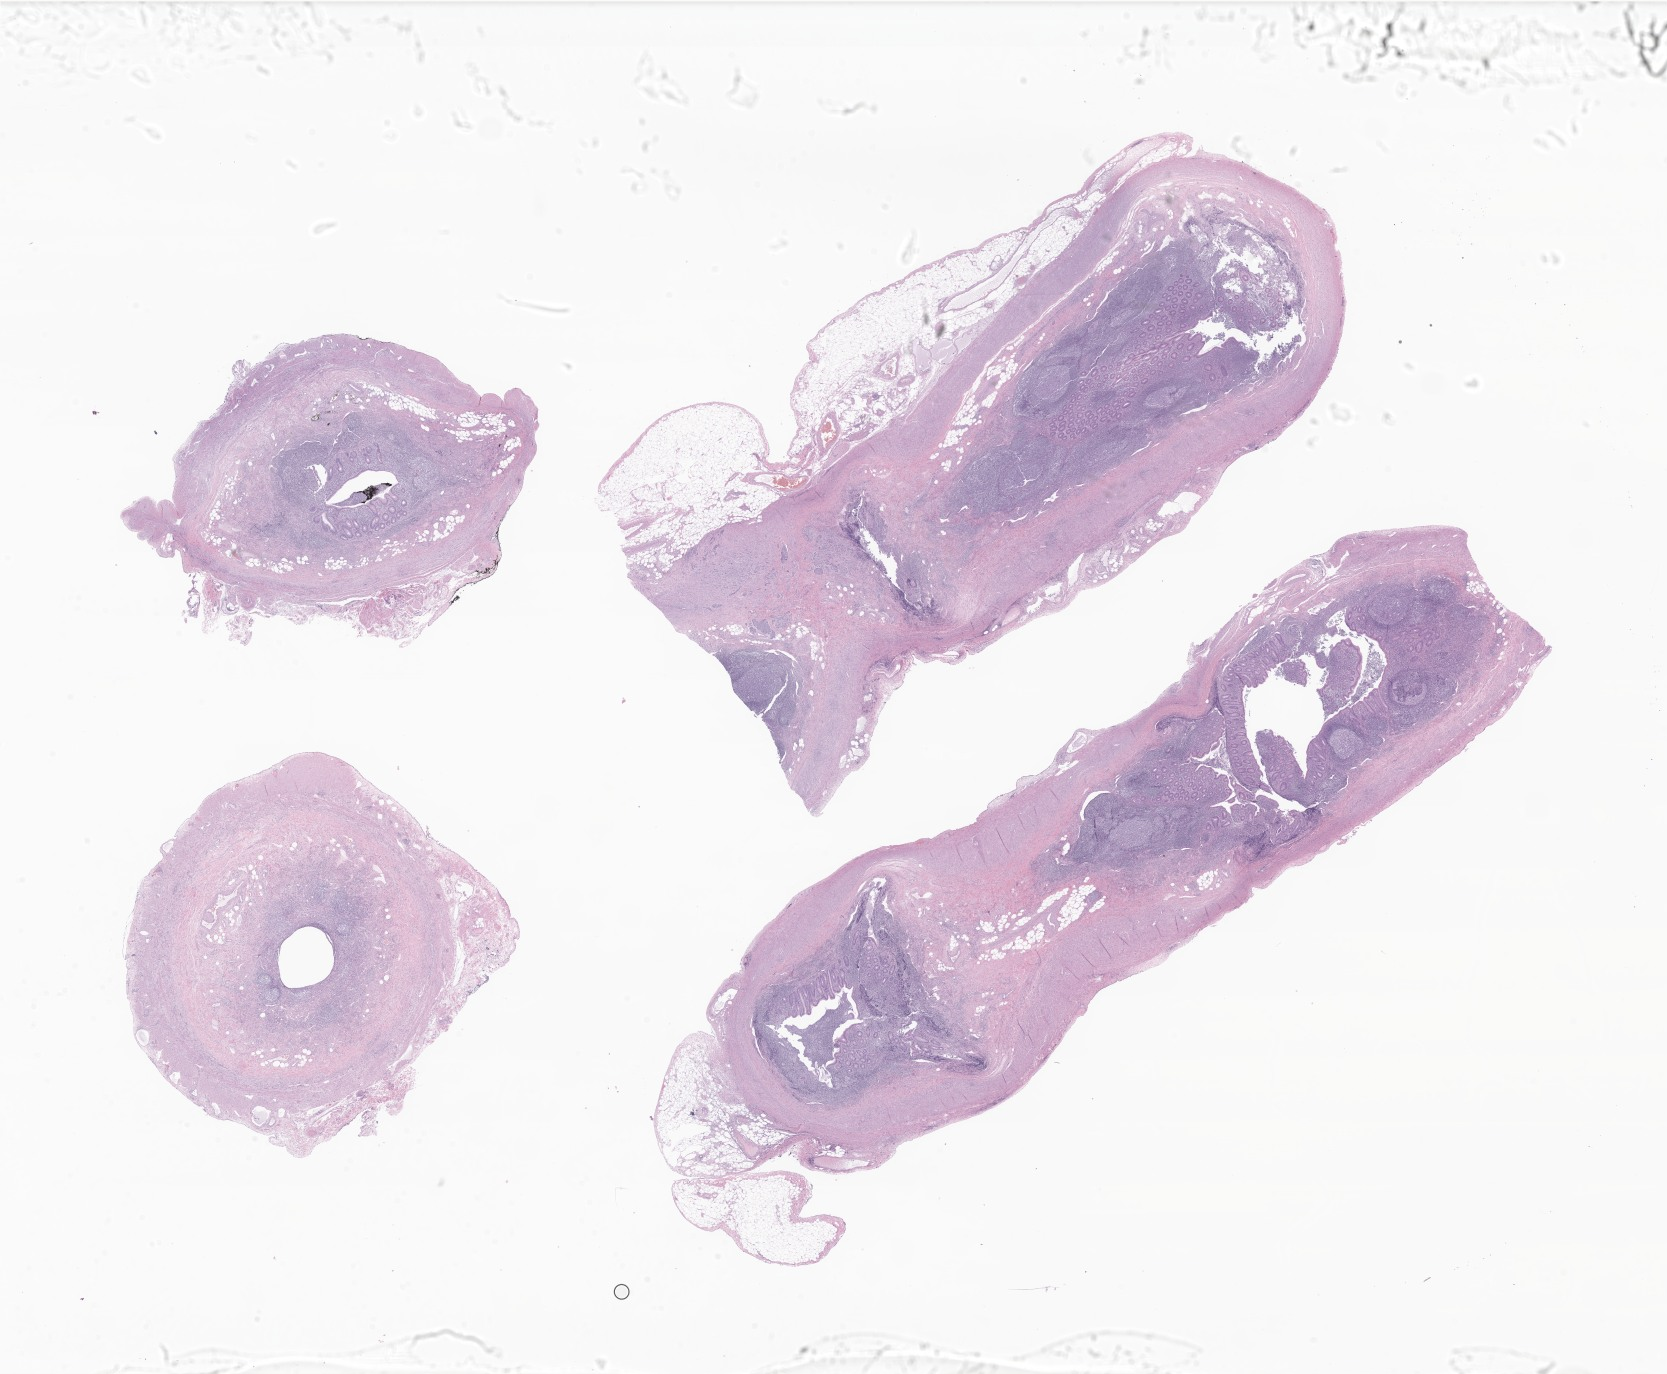
Whole-slide image, hematoxylin and eosin (H&E) stain of tumor tissue from the appendix — low-resolution overview of the scanned area, about 28.1 x 23.2 mm. Formalin-fixed paraffin-embedded section. Patient female; age 170 months (14 years 2 months).
- recorded diagnosis: Carcinoid tumor of uncertain malignant potential